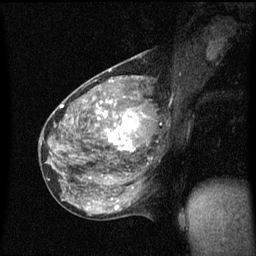
Breast MRI (dynamic contrast-enhanced), one sagittal slice; slice 27 of 60 in the series (ordered by position); dynamic contrast-enhanced series, image 2 of 3 at this slice position (ordered by acquisition); 1.5 T; TE 4.2 ms, TR 8.4 ms; 2 mm slice thickness; 256 × 256 image matrix, field of view 200 × 200 mm. Female patient, age 49 years.
Structures marked on this image (semi-automatic segmentation, software-assisted and operator-edited):
- analysis volume of interest (the breast-tissue region the enhancement analysis was run in; not a lesion): bounding box [x1, y1, x2, y2] px = [103, 90, 157, 151]
- tumour enhancement mask (voxels above the 70 % enhancement threshold inside the analysis volume of interest): [105, 100, 140, 151]